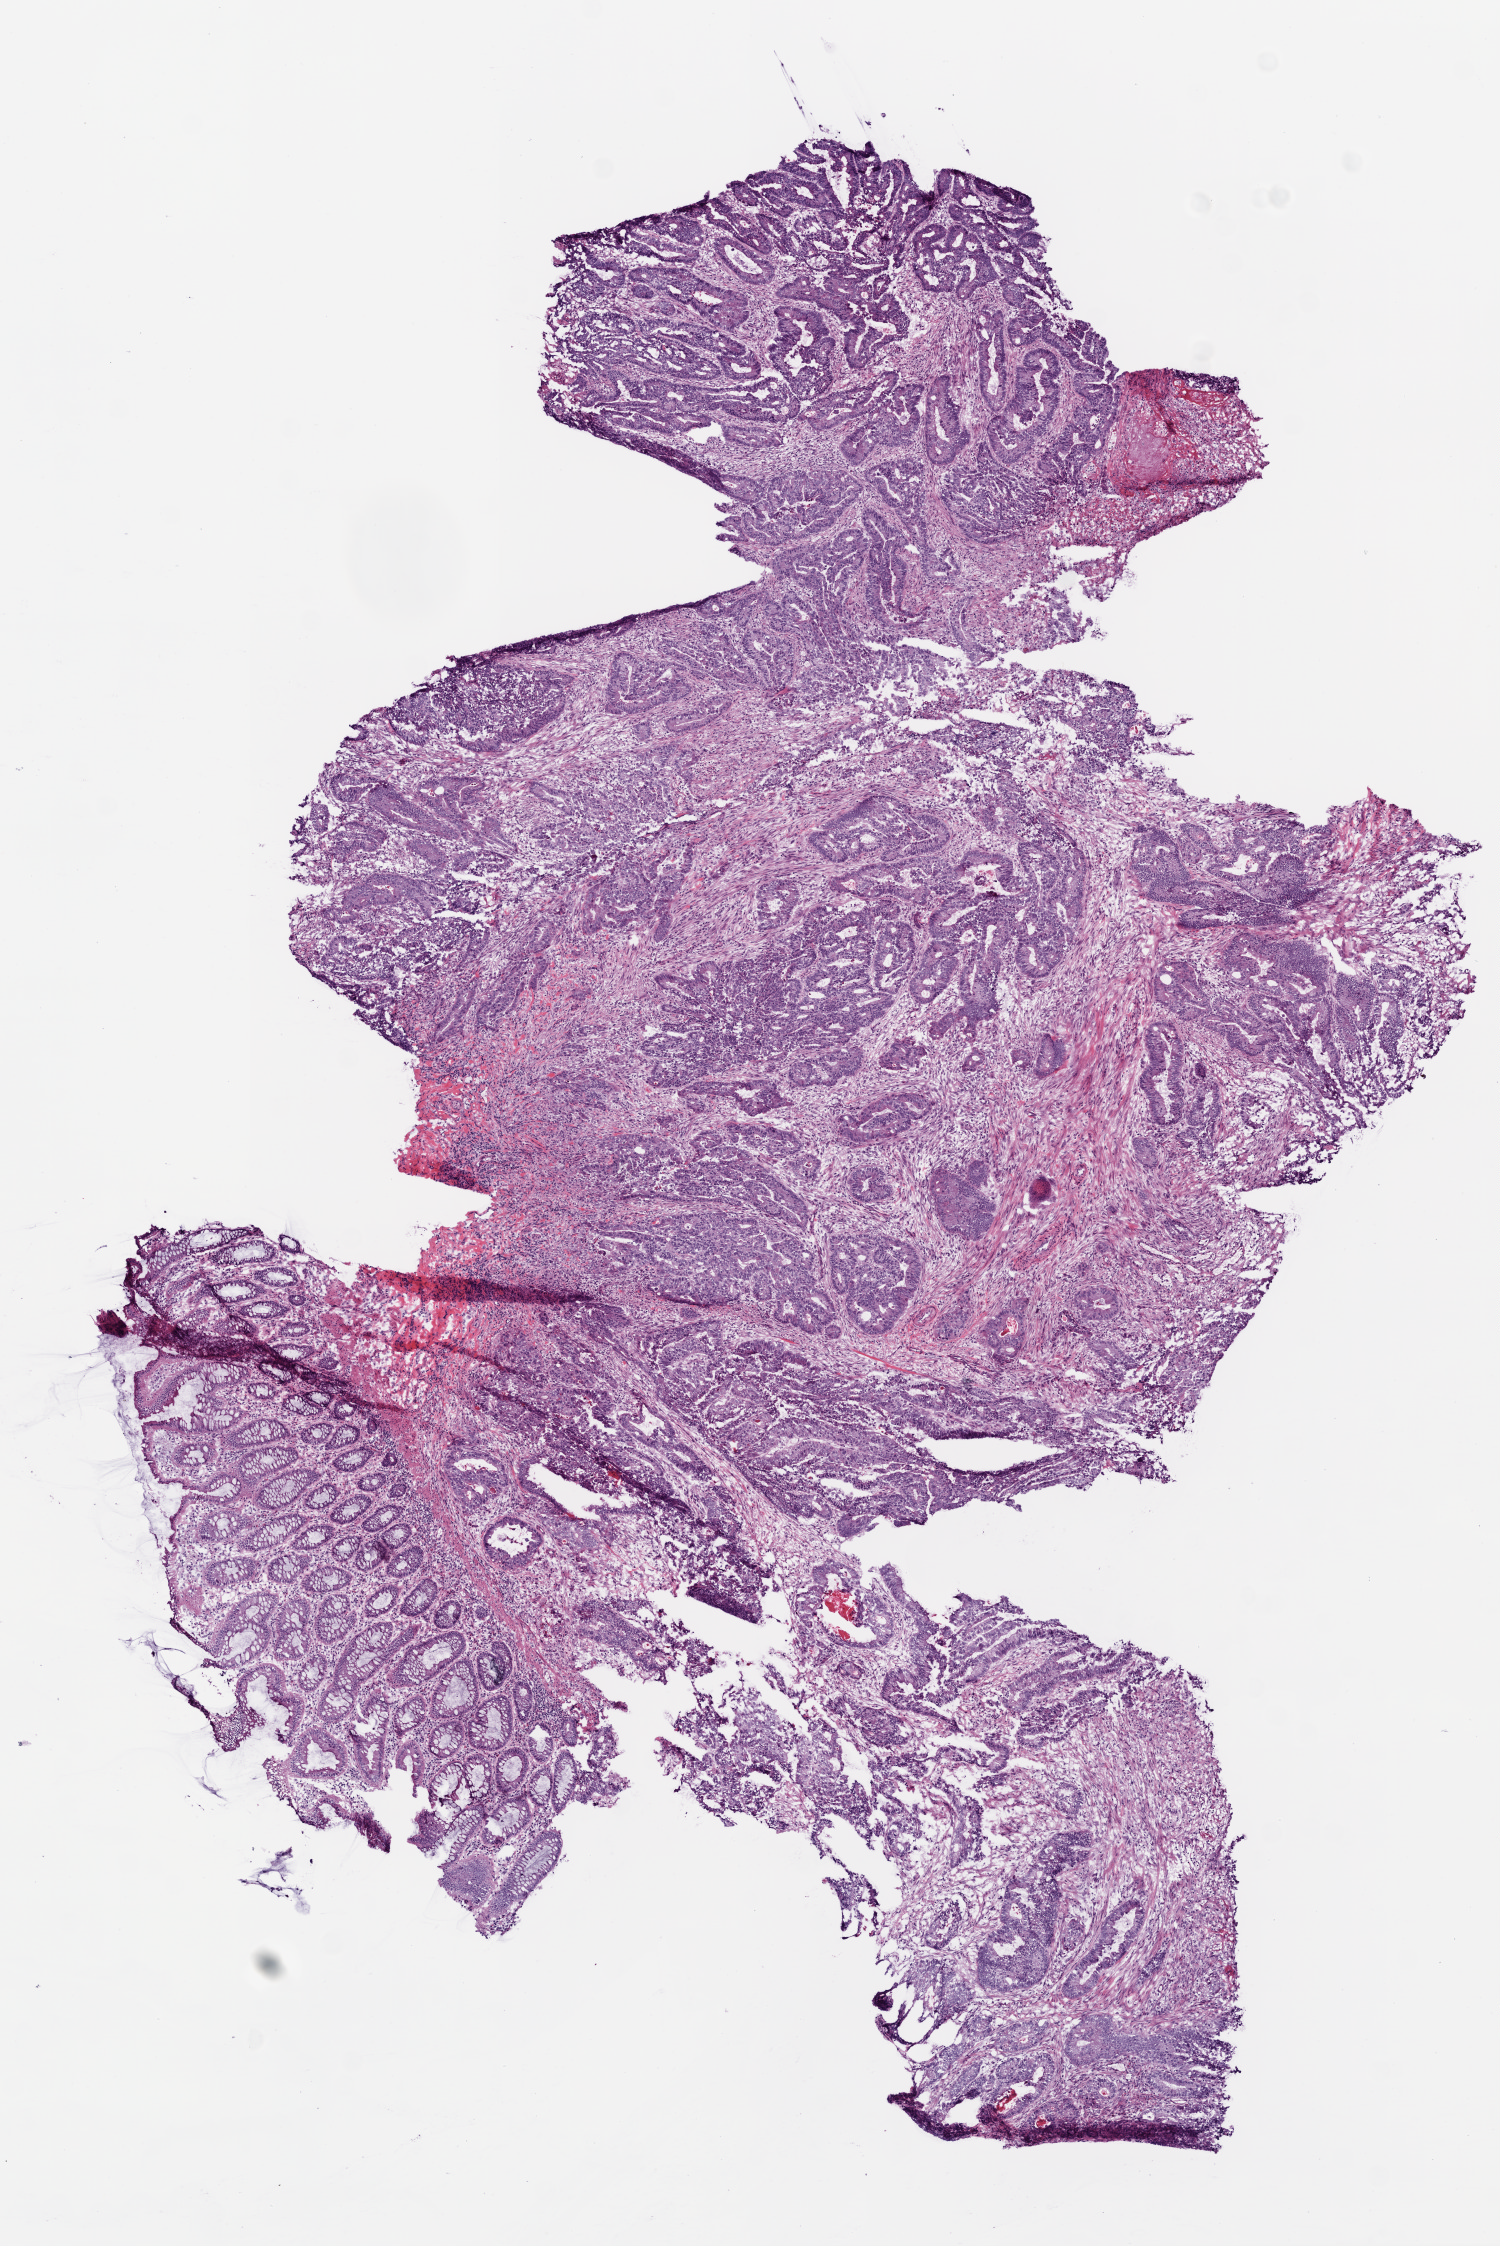
Whole-slide histology image, H&E-stained, shown as a low-resolution overview of the whole scanned area (about 6.0 x 9.0 mm, from a 20x scan), frozen section, sample: primary tumour, rectum. Female, age 59 years at initial diagnosis. Composition of this section per pathologist review: tumour cells 67%, tumour nuclei 75%, normal cells 20%, stromal cells 10%, necrosis 3%.
TNM: T3 N0 M0. Histologic diagnosis: Adenocarcinoma, NOS. Lymph nodes positive (case pathology): 0 of 12 examined. AJCC pathologic stage: II.